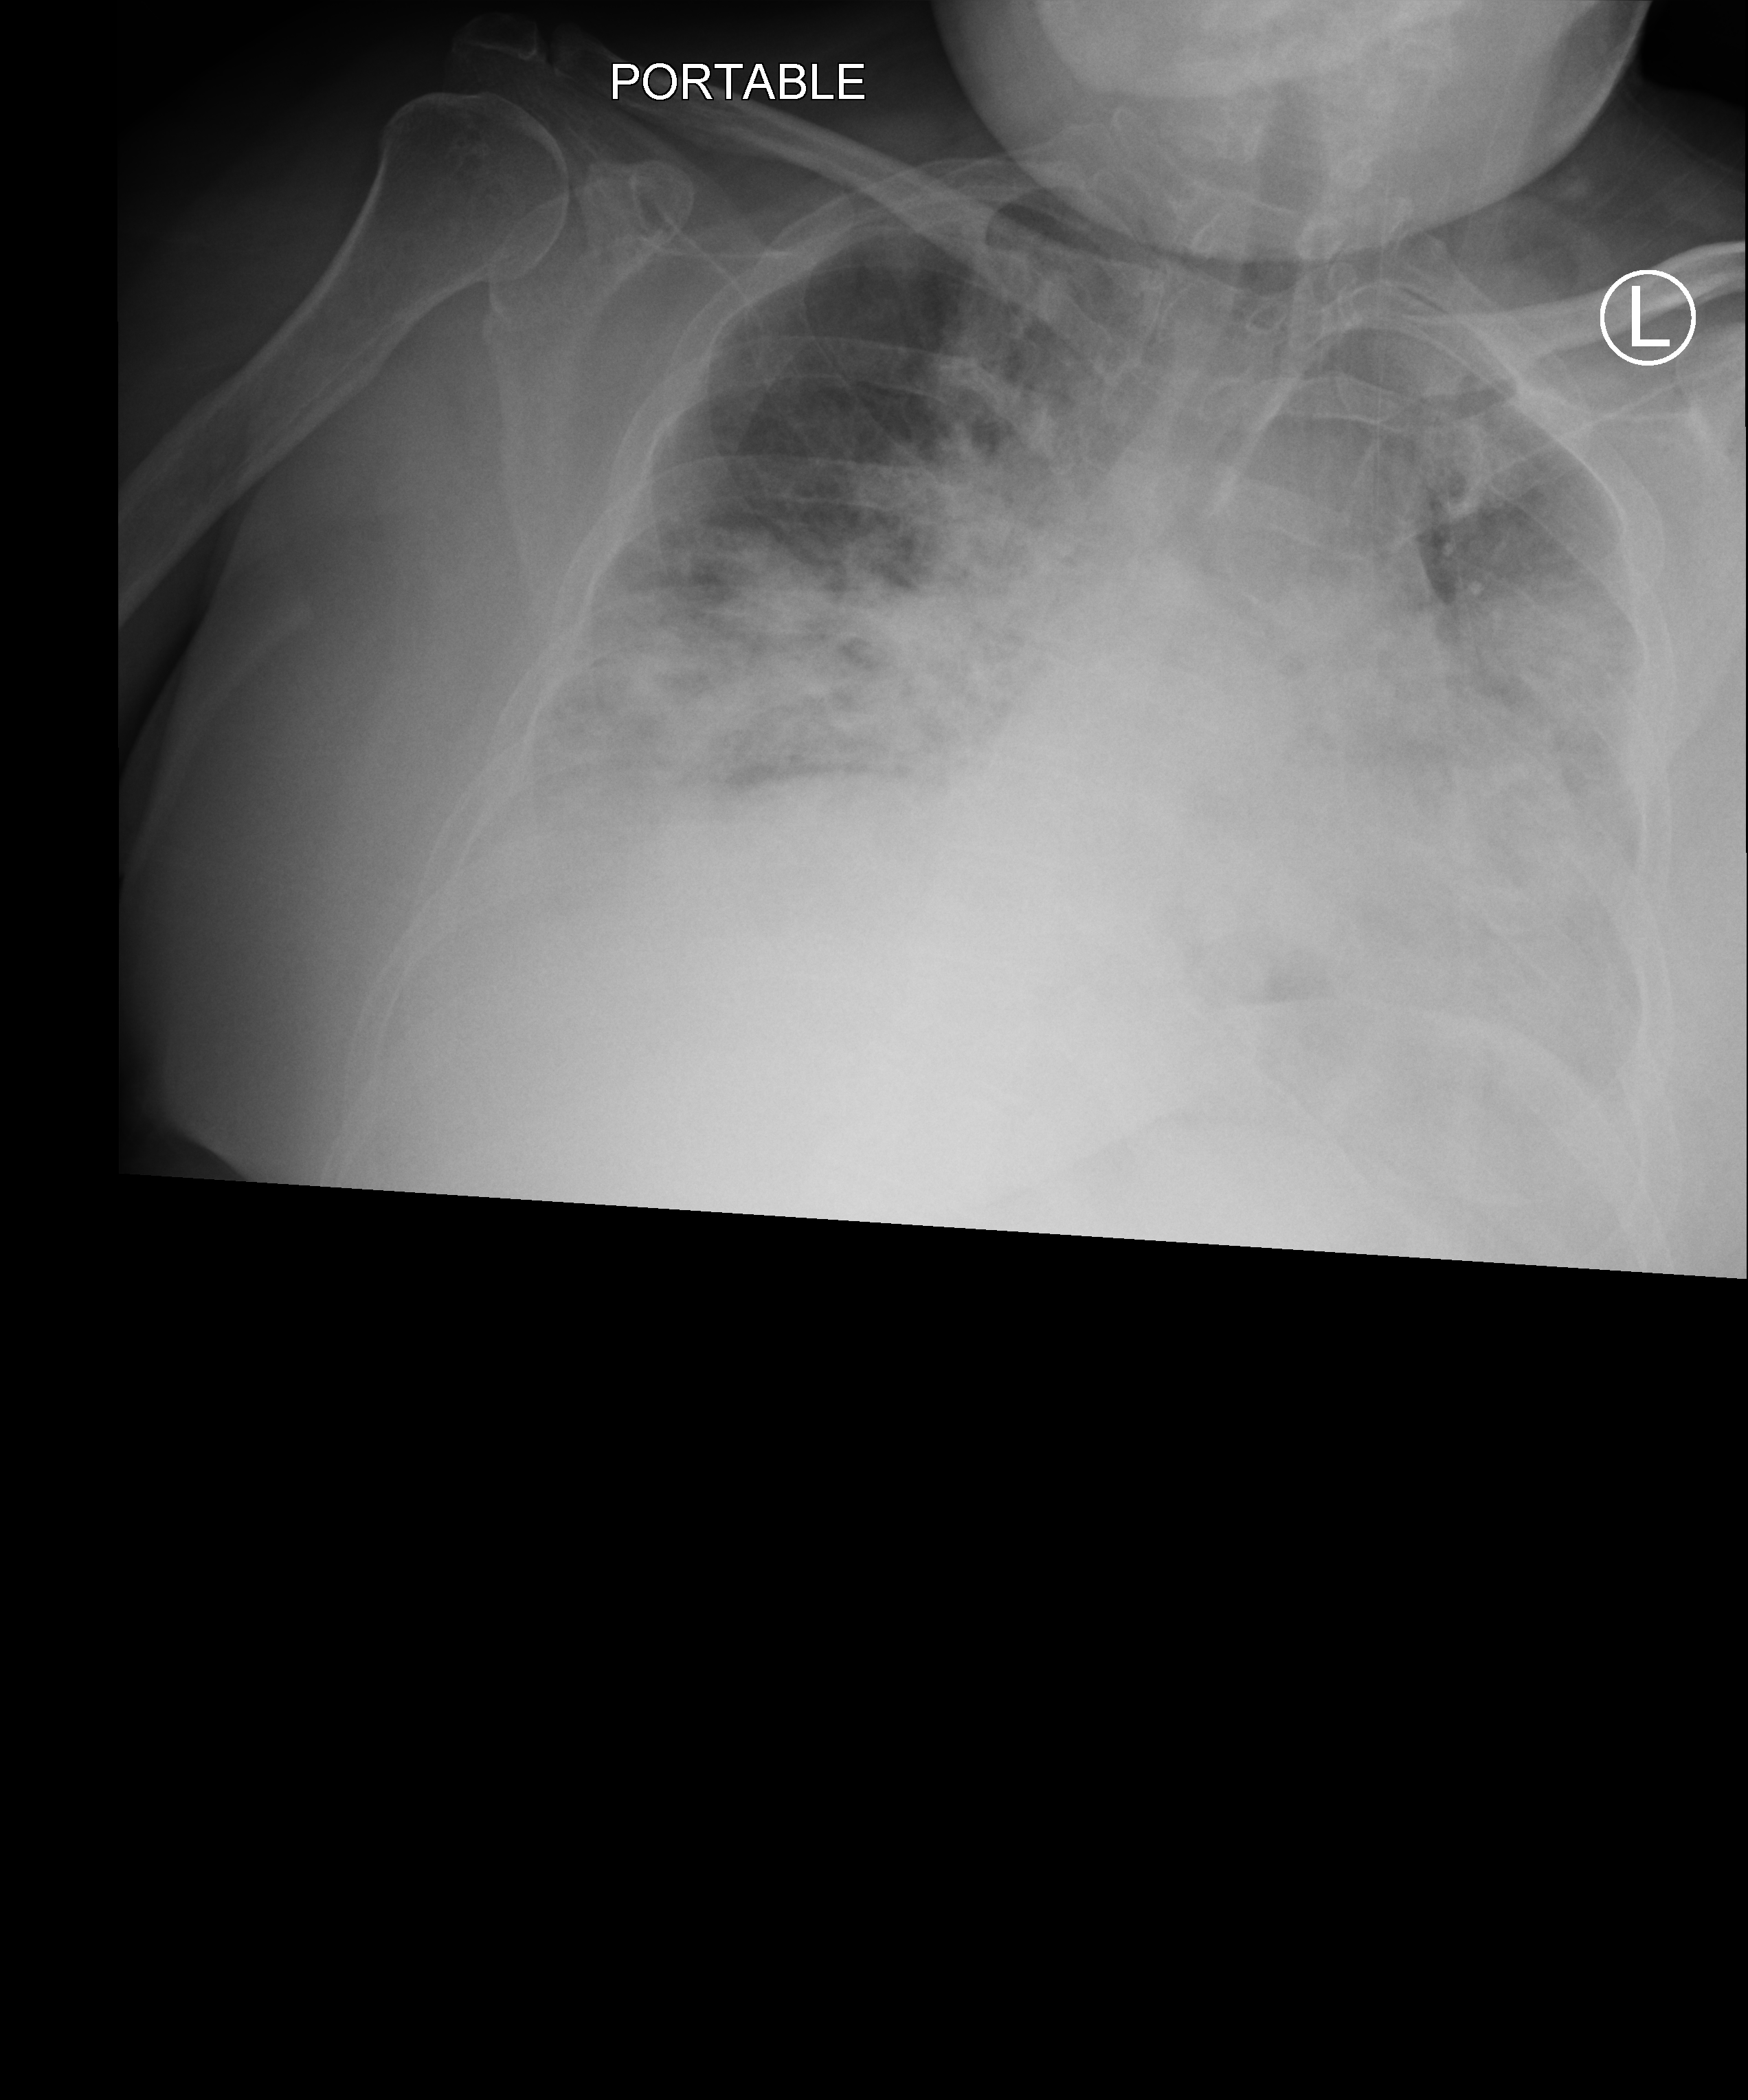
Chest X-ray (portable); anteroposterior (AP) projection. Patient hospitalised with COVID-19, aged 18–59 years.
From the hospital-stay record, not from the radiograph (when in the stay this image was taken is not recorded):
- length of hospital stay: 15 days
- admitted to intensive care during this hospital stay: yes